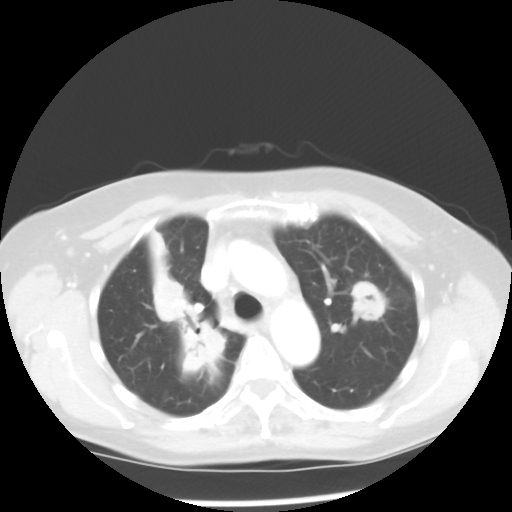
Chest CT, one axial slice; slice 36 of 52 in the series (ordered by position); 100 kVp; lung window (W 1500 / L -600 HU); 5 mm slice thickness; 512 × 512 image matrix, field of view 328 × 328 mm. Female patient, age 60 years. Case-level facts recorded for this patient, not image findings: clinical TNM (as recorded): T2 N1 M1a.
Outlined on this slice (rectangle marked by the reading radiologist):
- lung tumour (recorded histology: adenocarcinoma): box from (x=146, y=232) to (x=228, y=381) px